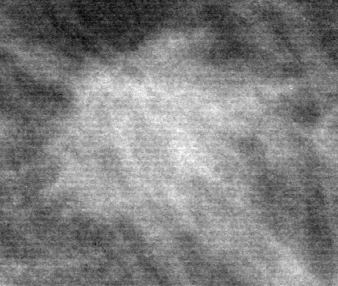
Crop from a digitized film mammogram around one marked abnormality; left breast; MLO view.
Mass, shape oval, margins spiculated; BI-RADS assessment category 5; subtlety rating 5 on a 1 (subtle) to 5 (obvious) scale; pathology result (as recorded, not read from the image): malignant.